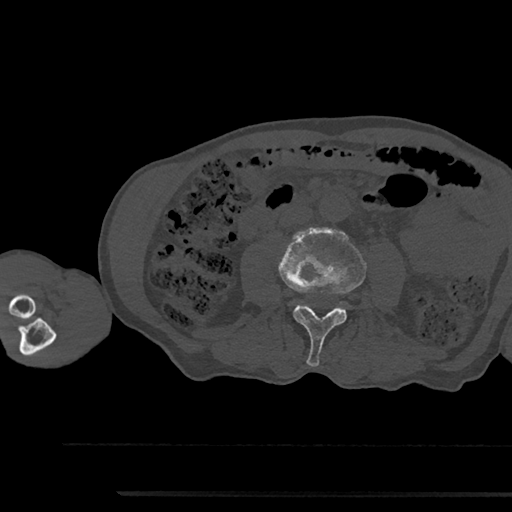
CT including the spine, one axial slice; 120 kVp; bone window (W 1800 / L 400 HU); 0.5 mm slice thickness; 512 × 512 image matrix, field of view 367 × 367 mm. Patient: male, 79 years. From the clinical record (not read from this slice): primary cancer: prostate.
Structures marked on this image (semi-automatic segmentation, software-assisted and operator-edited):
- L3 vertebra: bounding box (x1, y1, x2, y2) in pixels: (279, 228, 366, 367)